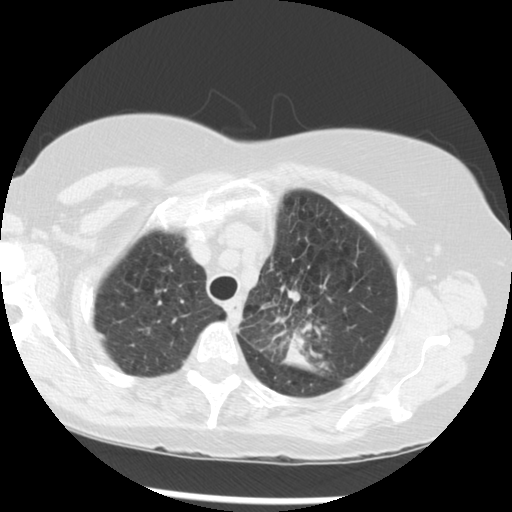
Low-dose screening chest CT, axial slice. Third screening round (two years after baseline). Lung window (W 1500 / L -600 HU). 2.5 mm slice thickness. Standard (soft-tissue) reconstruction kernel (STANDARD). Slice 232 of 283 in the series. 512 × 512 image matrix. Female participant, aged 70 years at enrolment. Current smoker at enrolment.
- Expert-annotated lung lesion, bounding box (x1, y1, x2, y2) in pixels: (254, 282, 351, 370).
- Screening reader's record for this exam (one nodule recorded; not confirmed to be the boxed lesion): non-calcified nodule or mass ≥4 mm, left upper lobe, 32 × 26 mm, spiculated (stellate) margins, soft tissue attenuation, pre-existing on the prior screen: yes; interval growth: yes.
- Official screen result: positive, other.
- Participant outcome: lung cancer diagnosed 24 days after this screen — neoplasm, malignant, left upper lobe, stage IIIB (AJCC 6th edition), 40 mm at pathology.